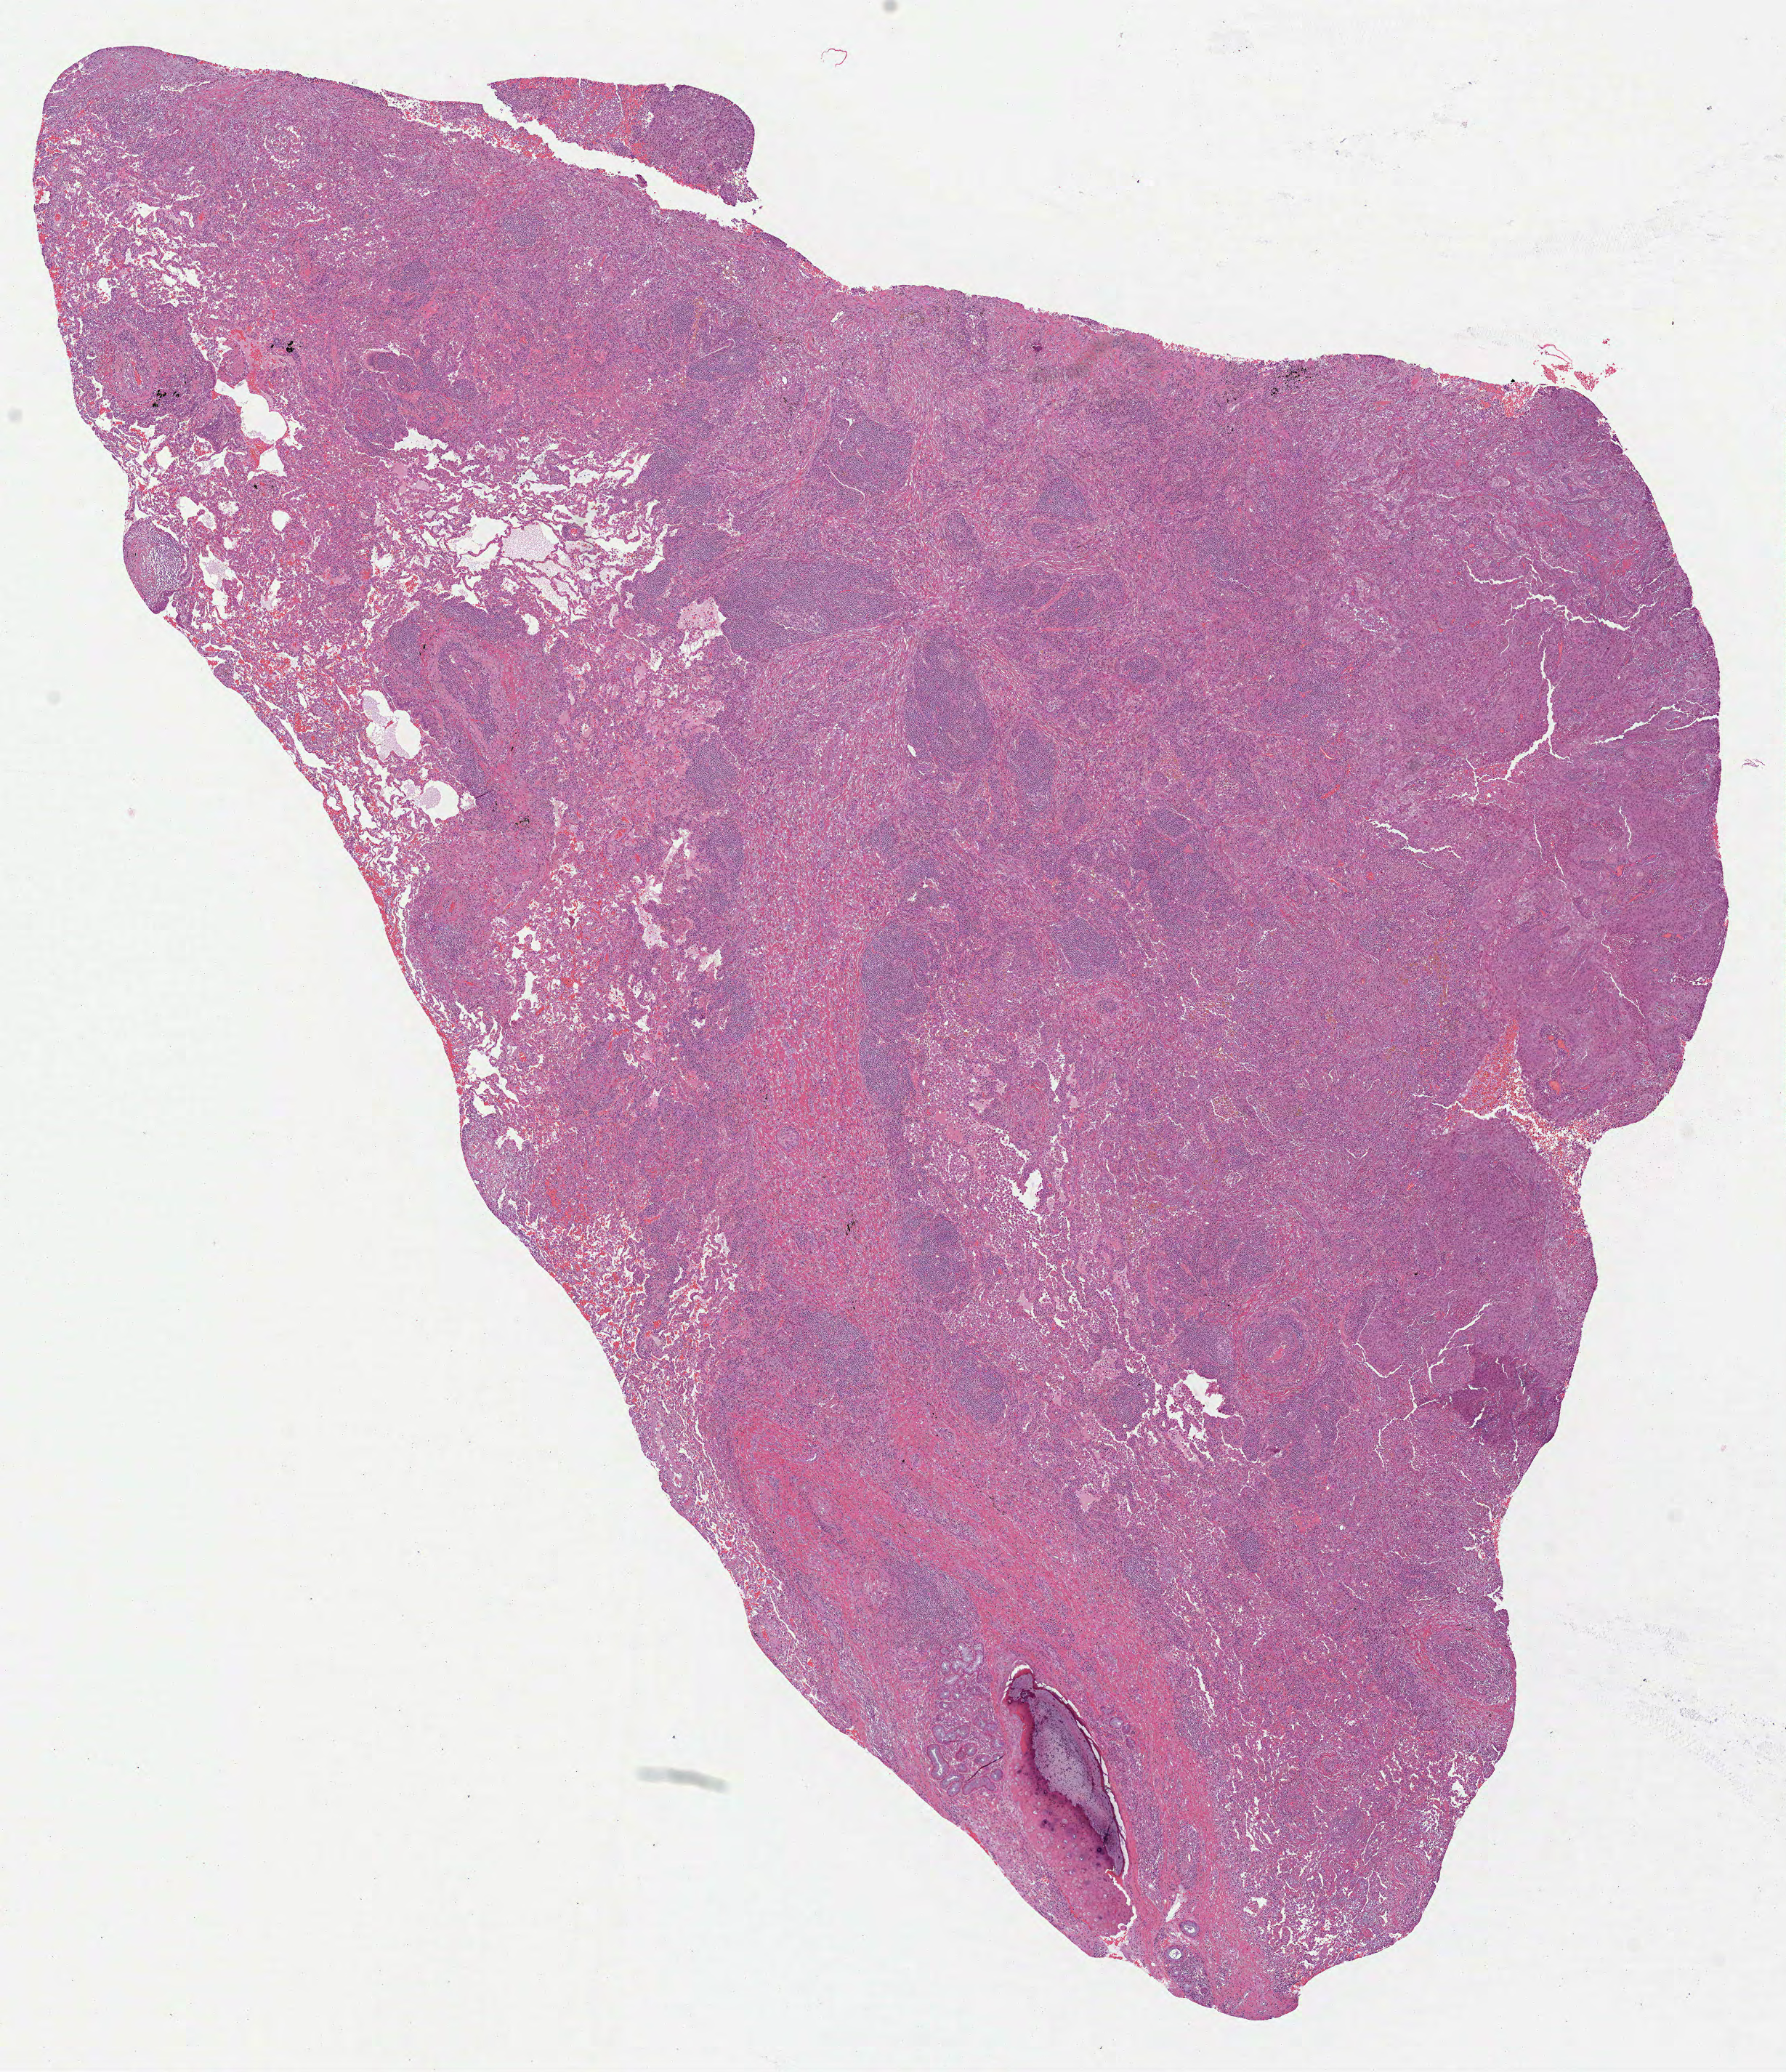
Digitized Hematoxylin and eosin (H&E) stained tissue section (whole slide), shown as a low-resolution overview of the whole scanned area (about 9.9 x 11.5 mm, slide scanned at 40x); FFPE section; primary tumour sample from the lung. Male patient; age at initial diagnosis 63 years.
• AJCC pathologic stage: IIA (7th edition)
• diagnosis: Squamous cell carcinoma, NOS (lower lobe, lung)